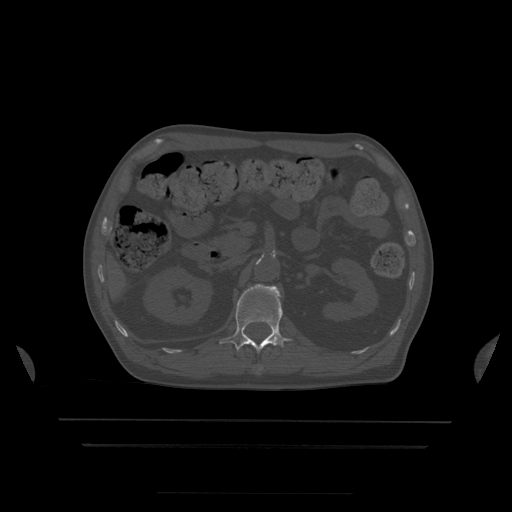
CT including the spine, one axial slice; position 171 of 522 along the scan axis; bone window (W 1800 / L 400 HU); 1.25 mm slice thickness; 512 × 512 image matrix, field of view 436 × 436 mm. Patient age 68 years. From the clinical record (not read from this slice): primary cancer: urothelial.
Structures marked on this image (semi-automatically segmented with operator editing):
- L1 vertebra: bounding box (x1, y1, x2, y2) in pixels: (220, 284, 292, 353)